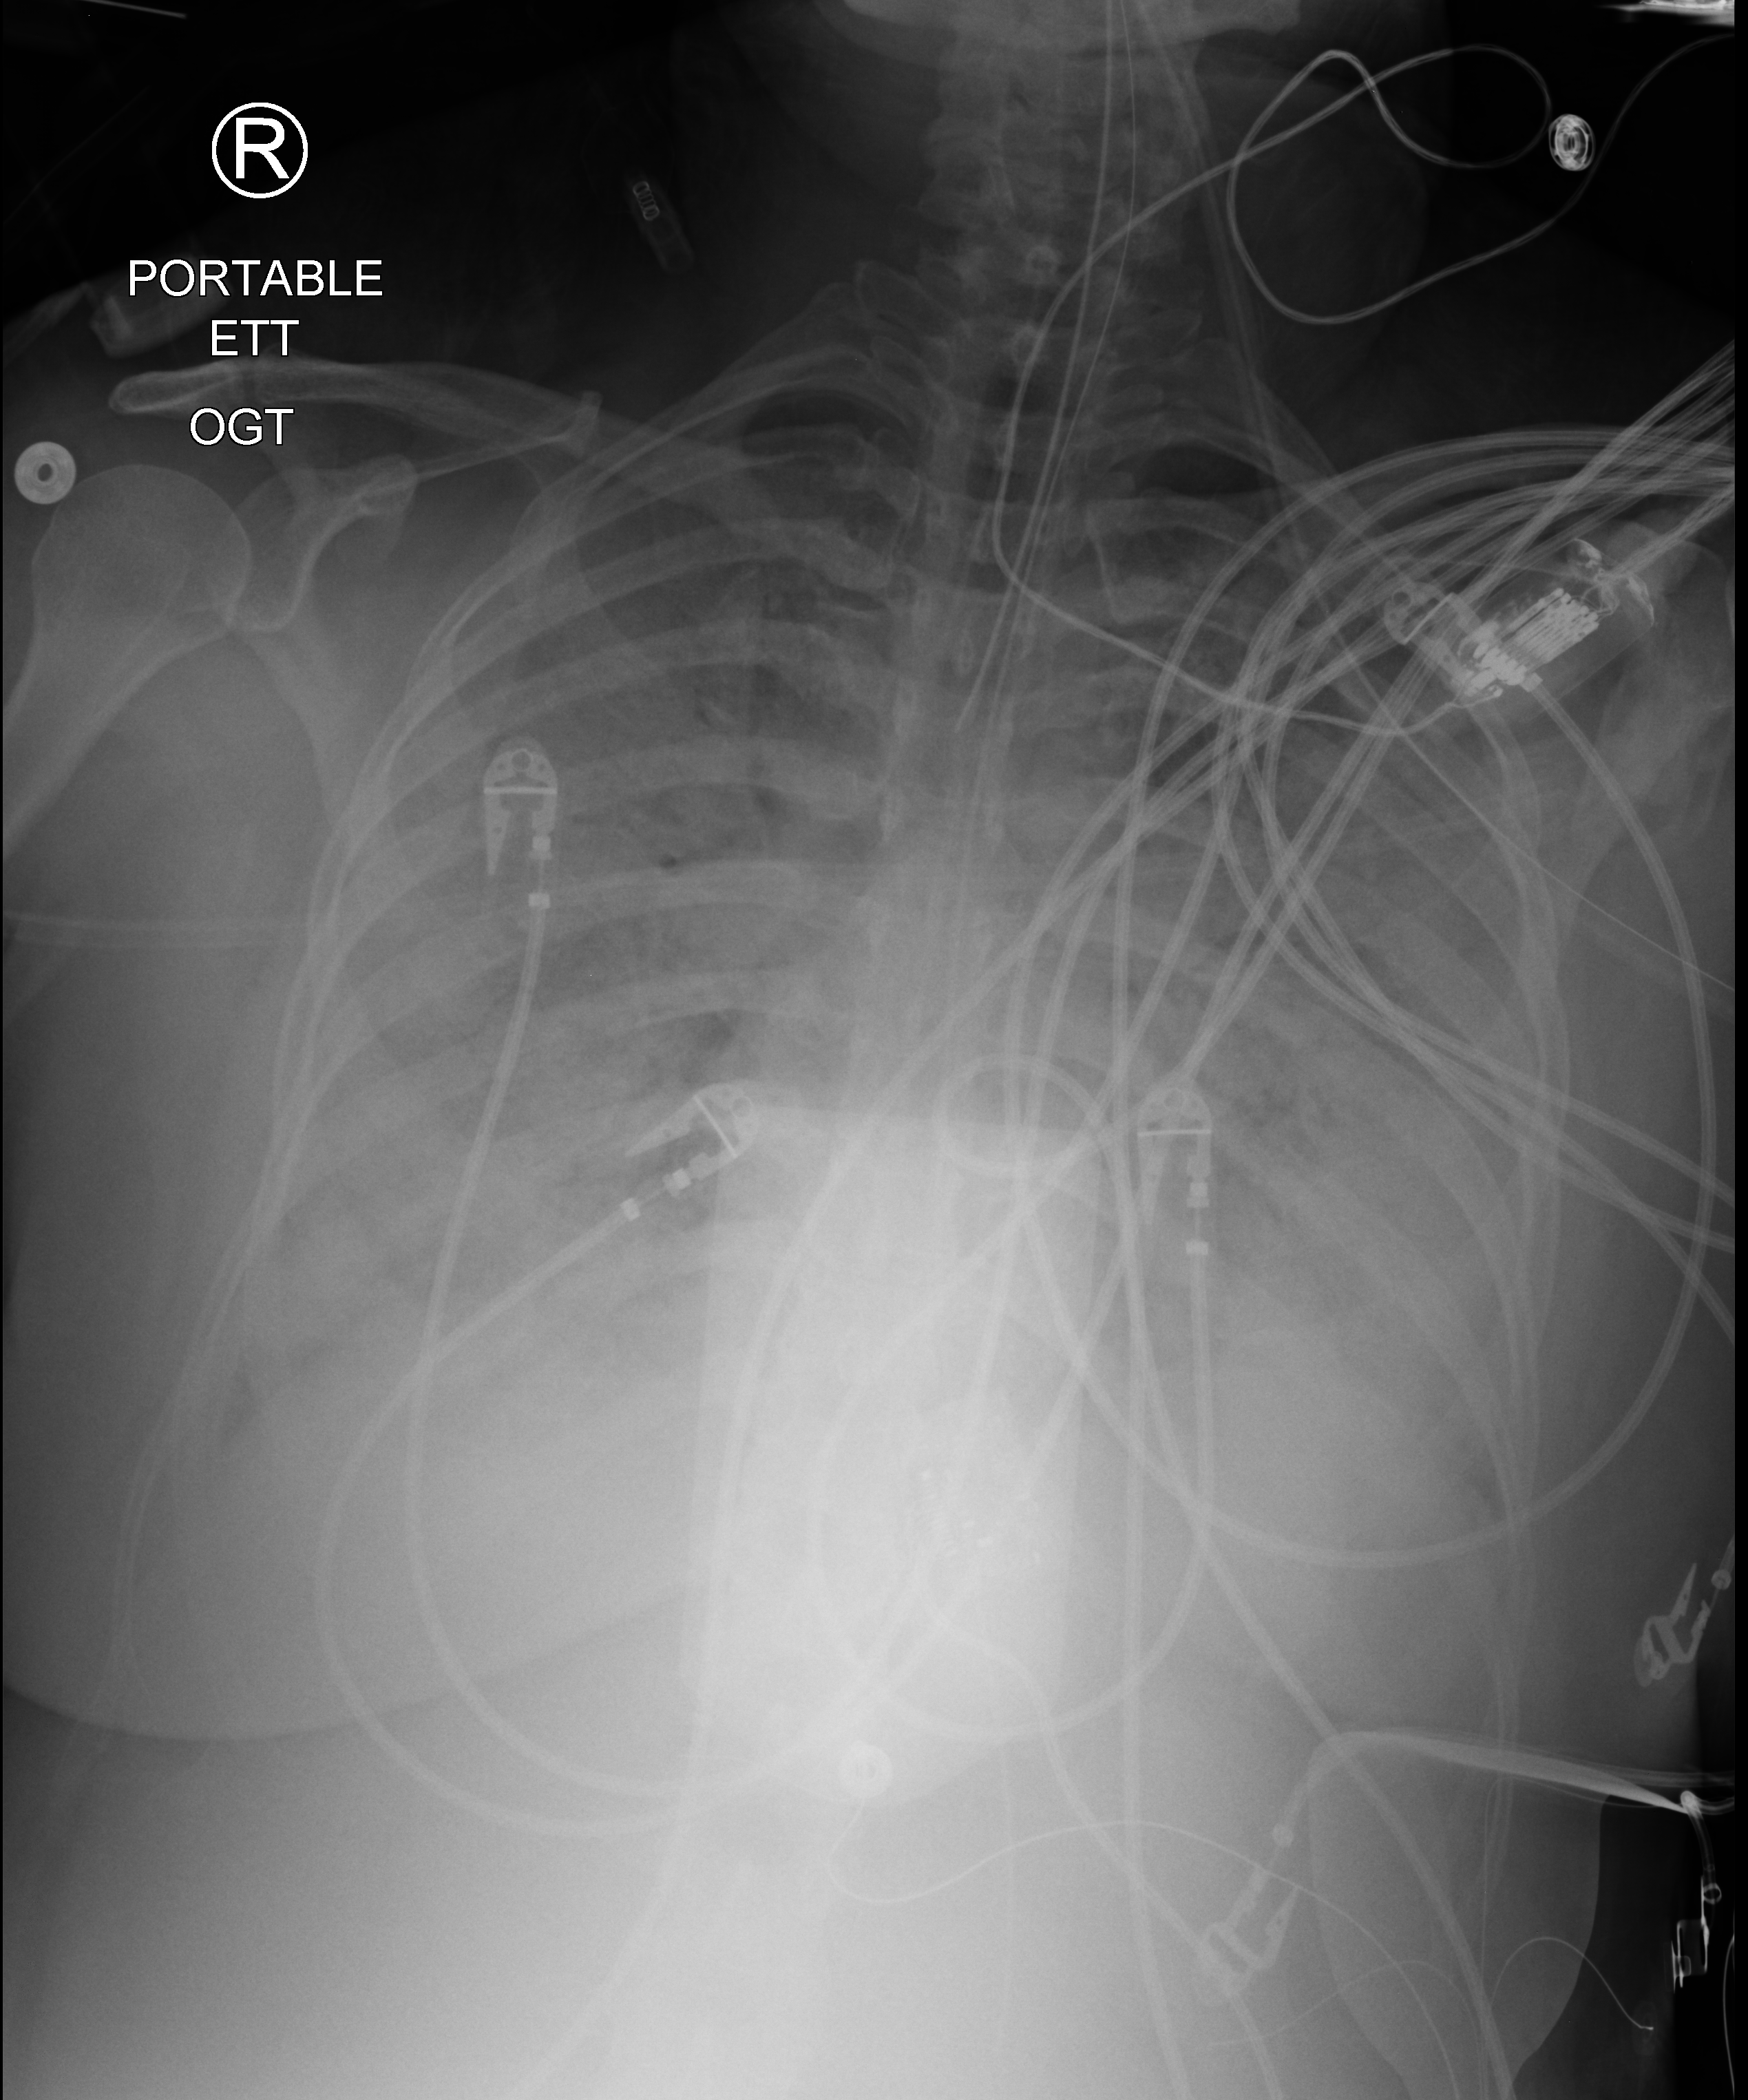
Bedside chest radiograph (computed radiography), anteroposterior (AP) projection. Patient hospitalised with COVID-19; male, aged 18–59 years.
Admission-level facts for this patient (not findings on this image; timing relative to this image not recorded): length of hospital stay: 38 days; diabetes (admission record): yes; admitted to intensive care during this hospital stay: yes.